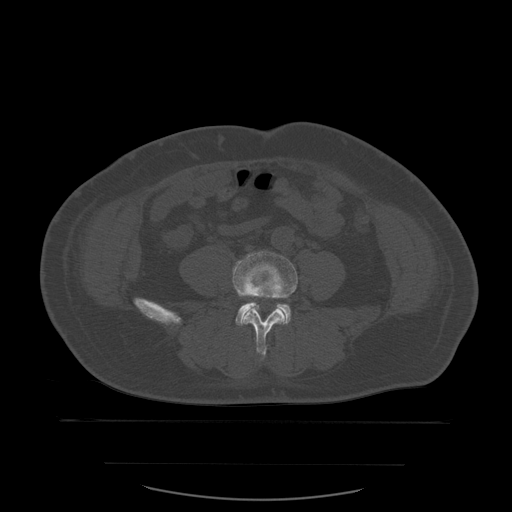
CT including the spine, one axial slice. Slice 156 of 590 in the series (ordered by position). Bone window (W 1800 / L 400 HU). 1.25 mm slice thickness. 512 × 512 image matrix, field of view 479 × 479 mm. Patient age 71 years. Case-level facts recorded for this patient, not image findings: primary cancer: lung; vertebrae with lytic lesions (as recorded): T1, T2, L5, S1.
Structures marked on this image (semi-automatic segmentation, software-assisted and operator-edited):
- L4 vertebra: bounding box [x1, y1, x2, y2] px = [233, 252, 298, 360]
- L5 vertebra: [236, 297, 291, 326]